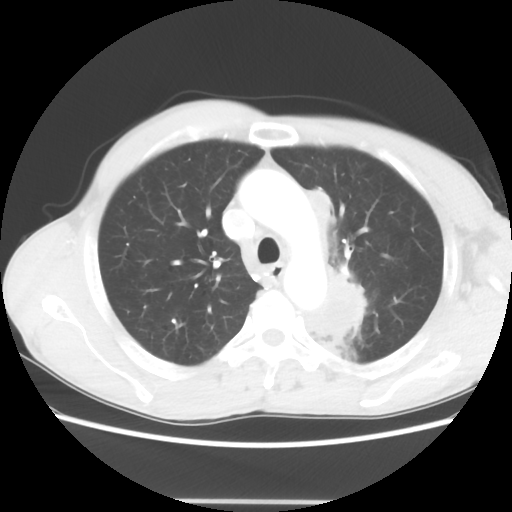
Chest CT, one axial slice; slice 47 of 62 in the series (ordered by position); reconstruction kernel STANDARD; lung window (W 1500 / L -600 HU); 5 mm slice thickness; 512 × 512 image matrix, field of view 360 × 360 mm. Patient: male, 61 years. Case-level facts recorded for this patient, not image findings: clinical TNM (as recorded): T3 N1 M1.
Annotated regions visible in this slice (bounding box drawn by a radiologist):
- lung tumour (recorded histology: adenocarcinoma): bounding box [x1, y1, x2, y2] px = [304, 260, 371, 358]
- lung tumour (recorded histology: adenocarcinoma): [309, 189, 342, 262]